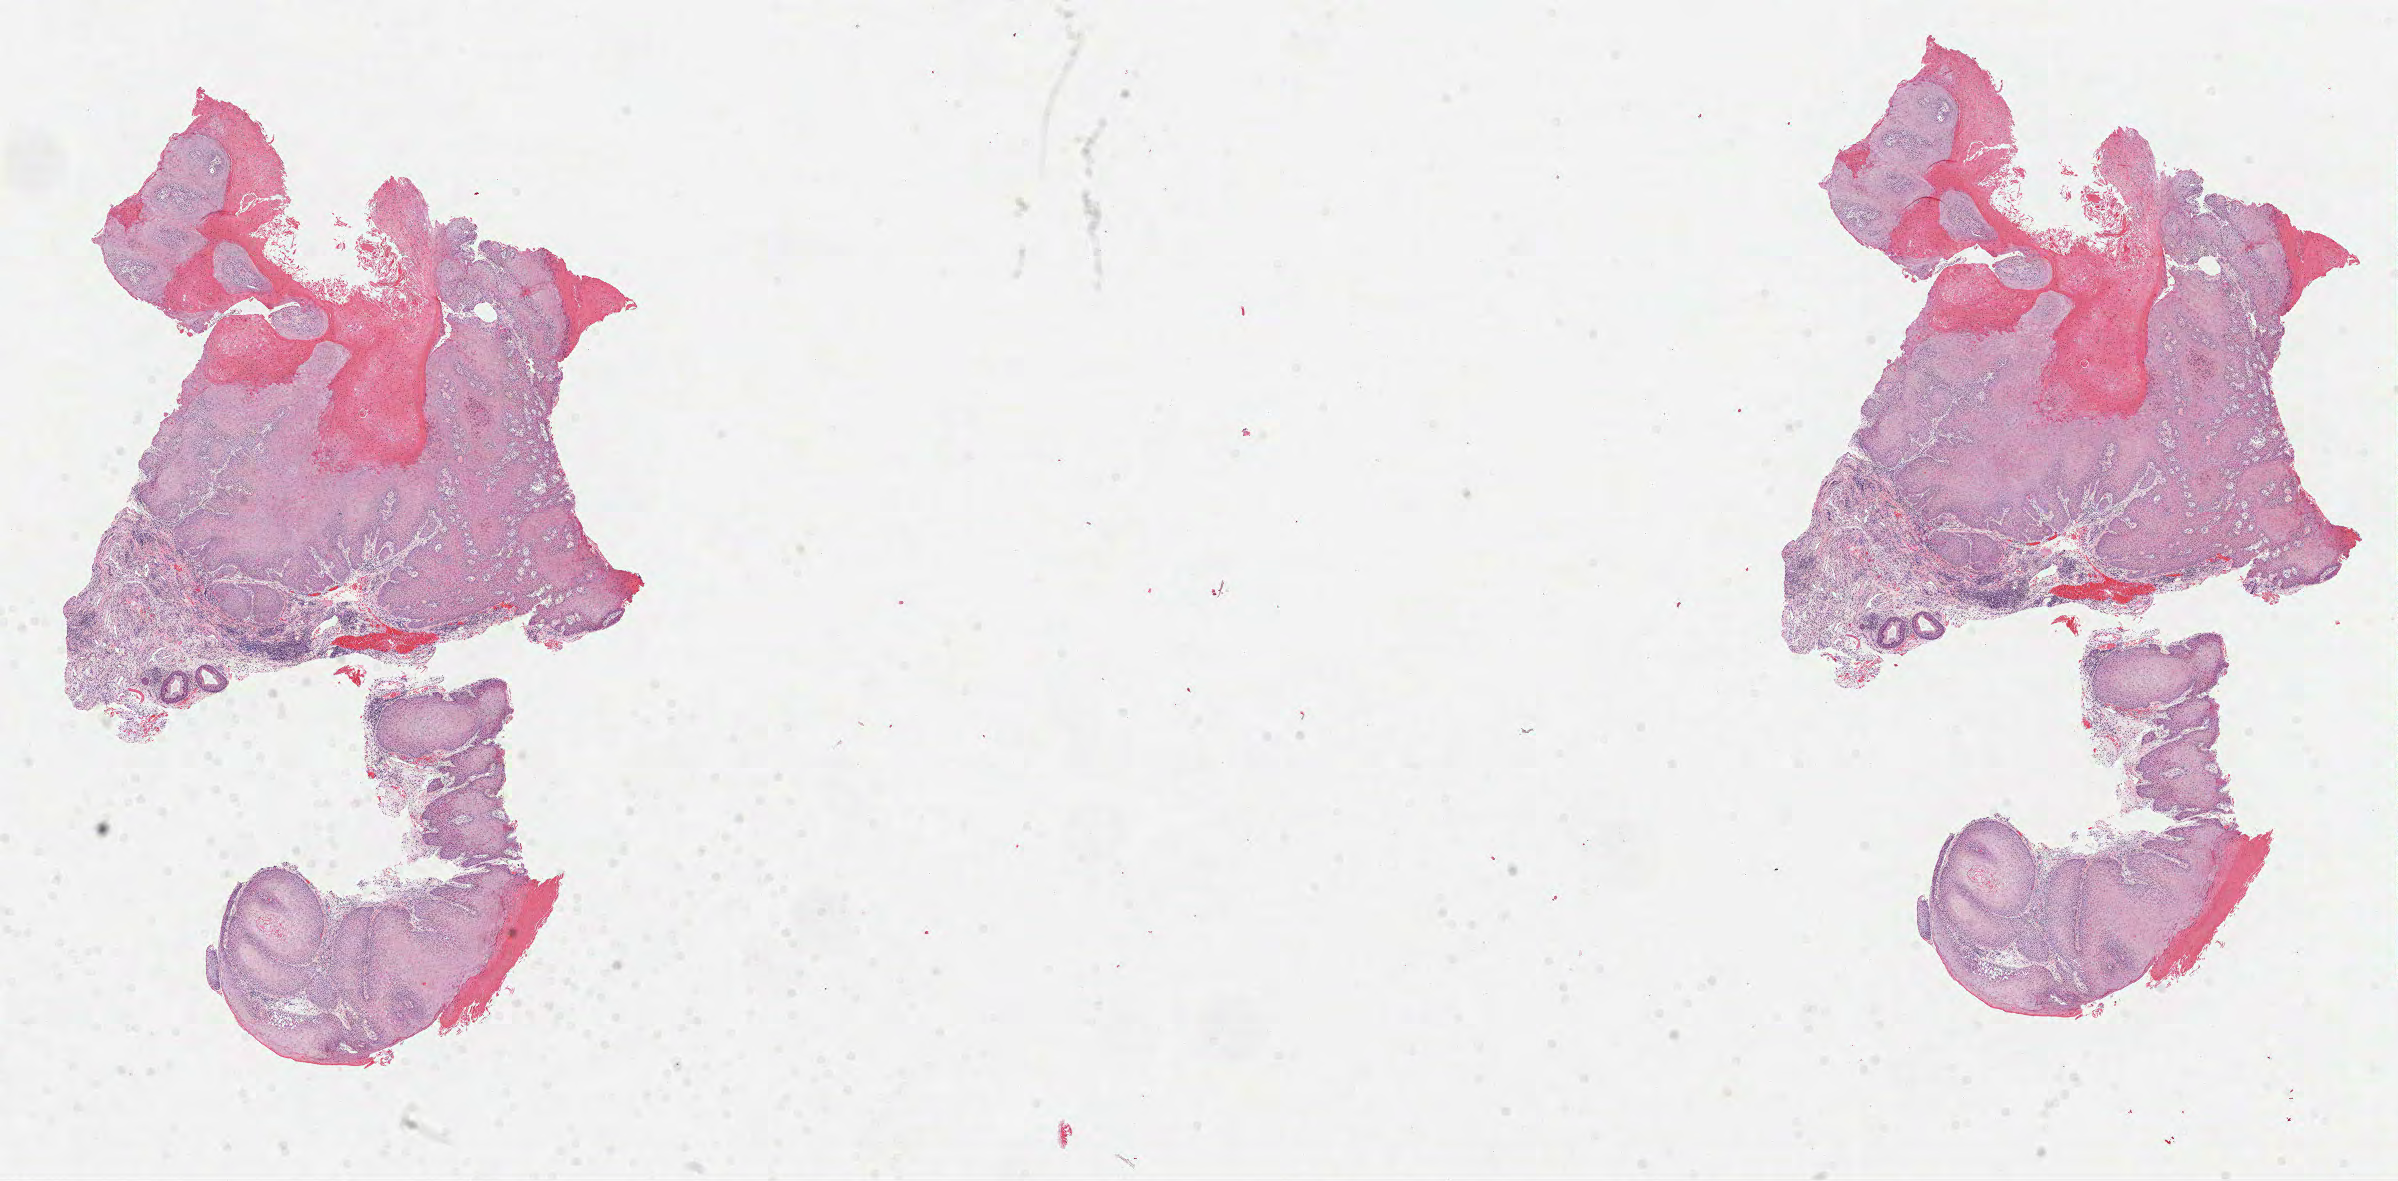
H&E whole-slide image — shown as a low-resolution overview of the whole scanned area (about 19.3 x 9.5 mm, slide scanned at 40x), FFPE section, primary tumour sample from the head and neck. Male, age 58 years at initial diagnosis. Histologic grade: G2 (moderately differentiated).
Histologic diagnosis: Squamous cell carcinoma, NOS (floor of mouth, NOS). AJCC pathologic stage: III (7th edition).